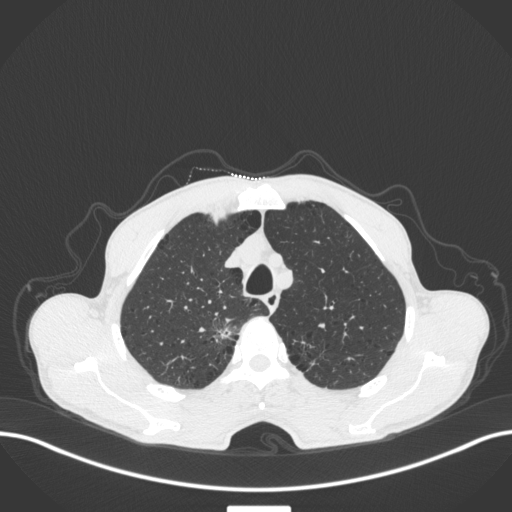
Chest CT, one axial slice. Position 345 of 445 along the scan axis. 120 kVp. Lung window (W 1500 / L -600 HU). 1 mm slice thickness. 512 × 512 image matrix, field of view 400 × 400 mm. Male patient, age 70 years. From the clinical record (not read from this slice): clinical TNM (as recorded): T1a N0 M0; histopathological grade: G1-2.
Annotated regions visible in this slice (rectangle marked by the reading radiologist):
- lung tumour (recorded histology: adenocarcinoma): bounding box <209,323,240,350> (left, top, right, bottom; pixels)